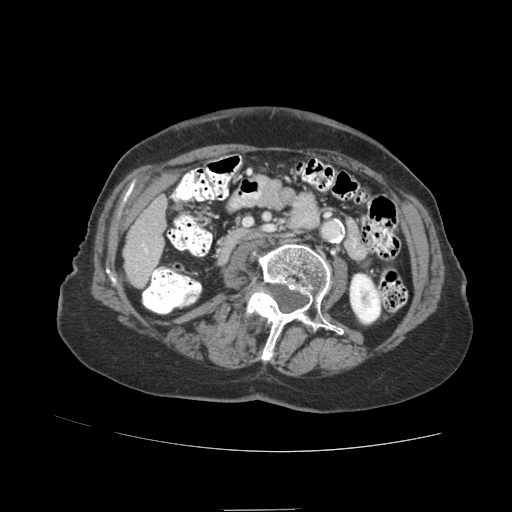
Contrast-enhanced abdominal CT (liver protocol), one axial slice. Position 17 of 89 along the scan axis. Reconstruction kernel STANDARD. 140 kVp. Soft-tissue window (W 400 / L 40 HU). 2.5 mm slice thickness. 512 × 512 image matrix. Case-level facts recorded for this patient, not image findings: diagnosis: hepatocellular carcinoma (patient treated with transarterial chemoembolisation; whether this scan precedes or follows treatment is not stated here); TNM stage (as recorded): Stage-II; Child-Pugh class: A; tumour differentiation: moderately differentiated; tumour nodularity: multinodular.
Annotated regions visible in this slice (semi-automatic segmentation, software-assisted and operator-edited):
- liver parenchyma outside the tumour (the mass and vessels are separate outlines, so this box may not span the whole liver): bounding box <124,180,166,288> (left, top, right, bottom; pixels)
- liver vessels: <144,248,148,254>